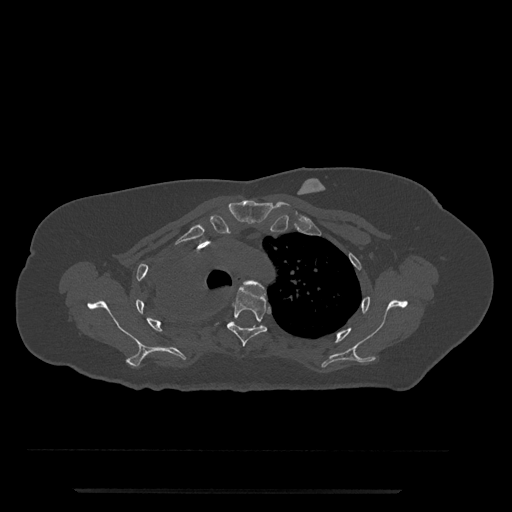
CT including the spine, one axial slice; slice 591 of 797 in the series (ordered by position); reconstruction kernel Br40s/3; 120 kVp; bone window (W 1800 / L 400 HU); 512 × 512 image matrix, field of view 440 × 440 mm. Patient: female, 51 years. From the clinical record (not read from this slice): primary cancer: neuro; vertebrae with lytic lesions (as recorded): T8.
Annotated regions visible in this slice (semi-automatically segmented with operator editing):
- T3 vertebra: bounding box <242,280,265,290> (left, top, right, bottom; pixels)
- T4 vertebra: <227,286,267,347>